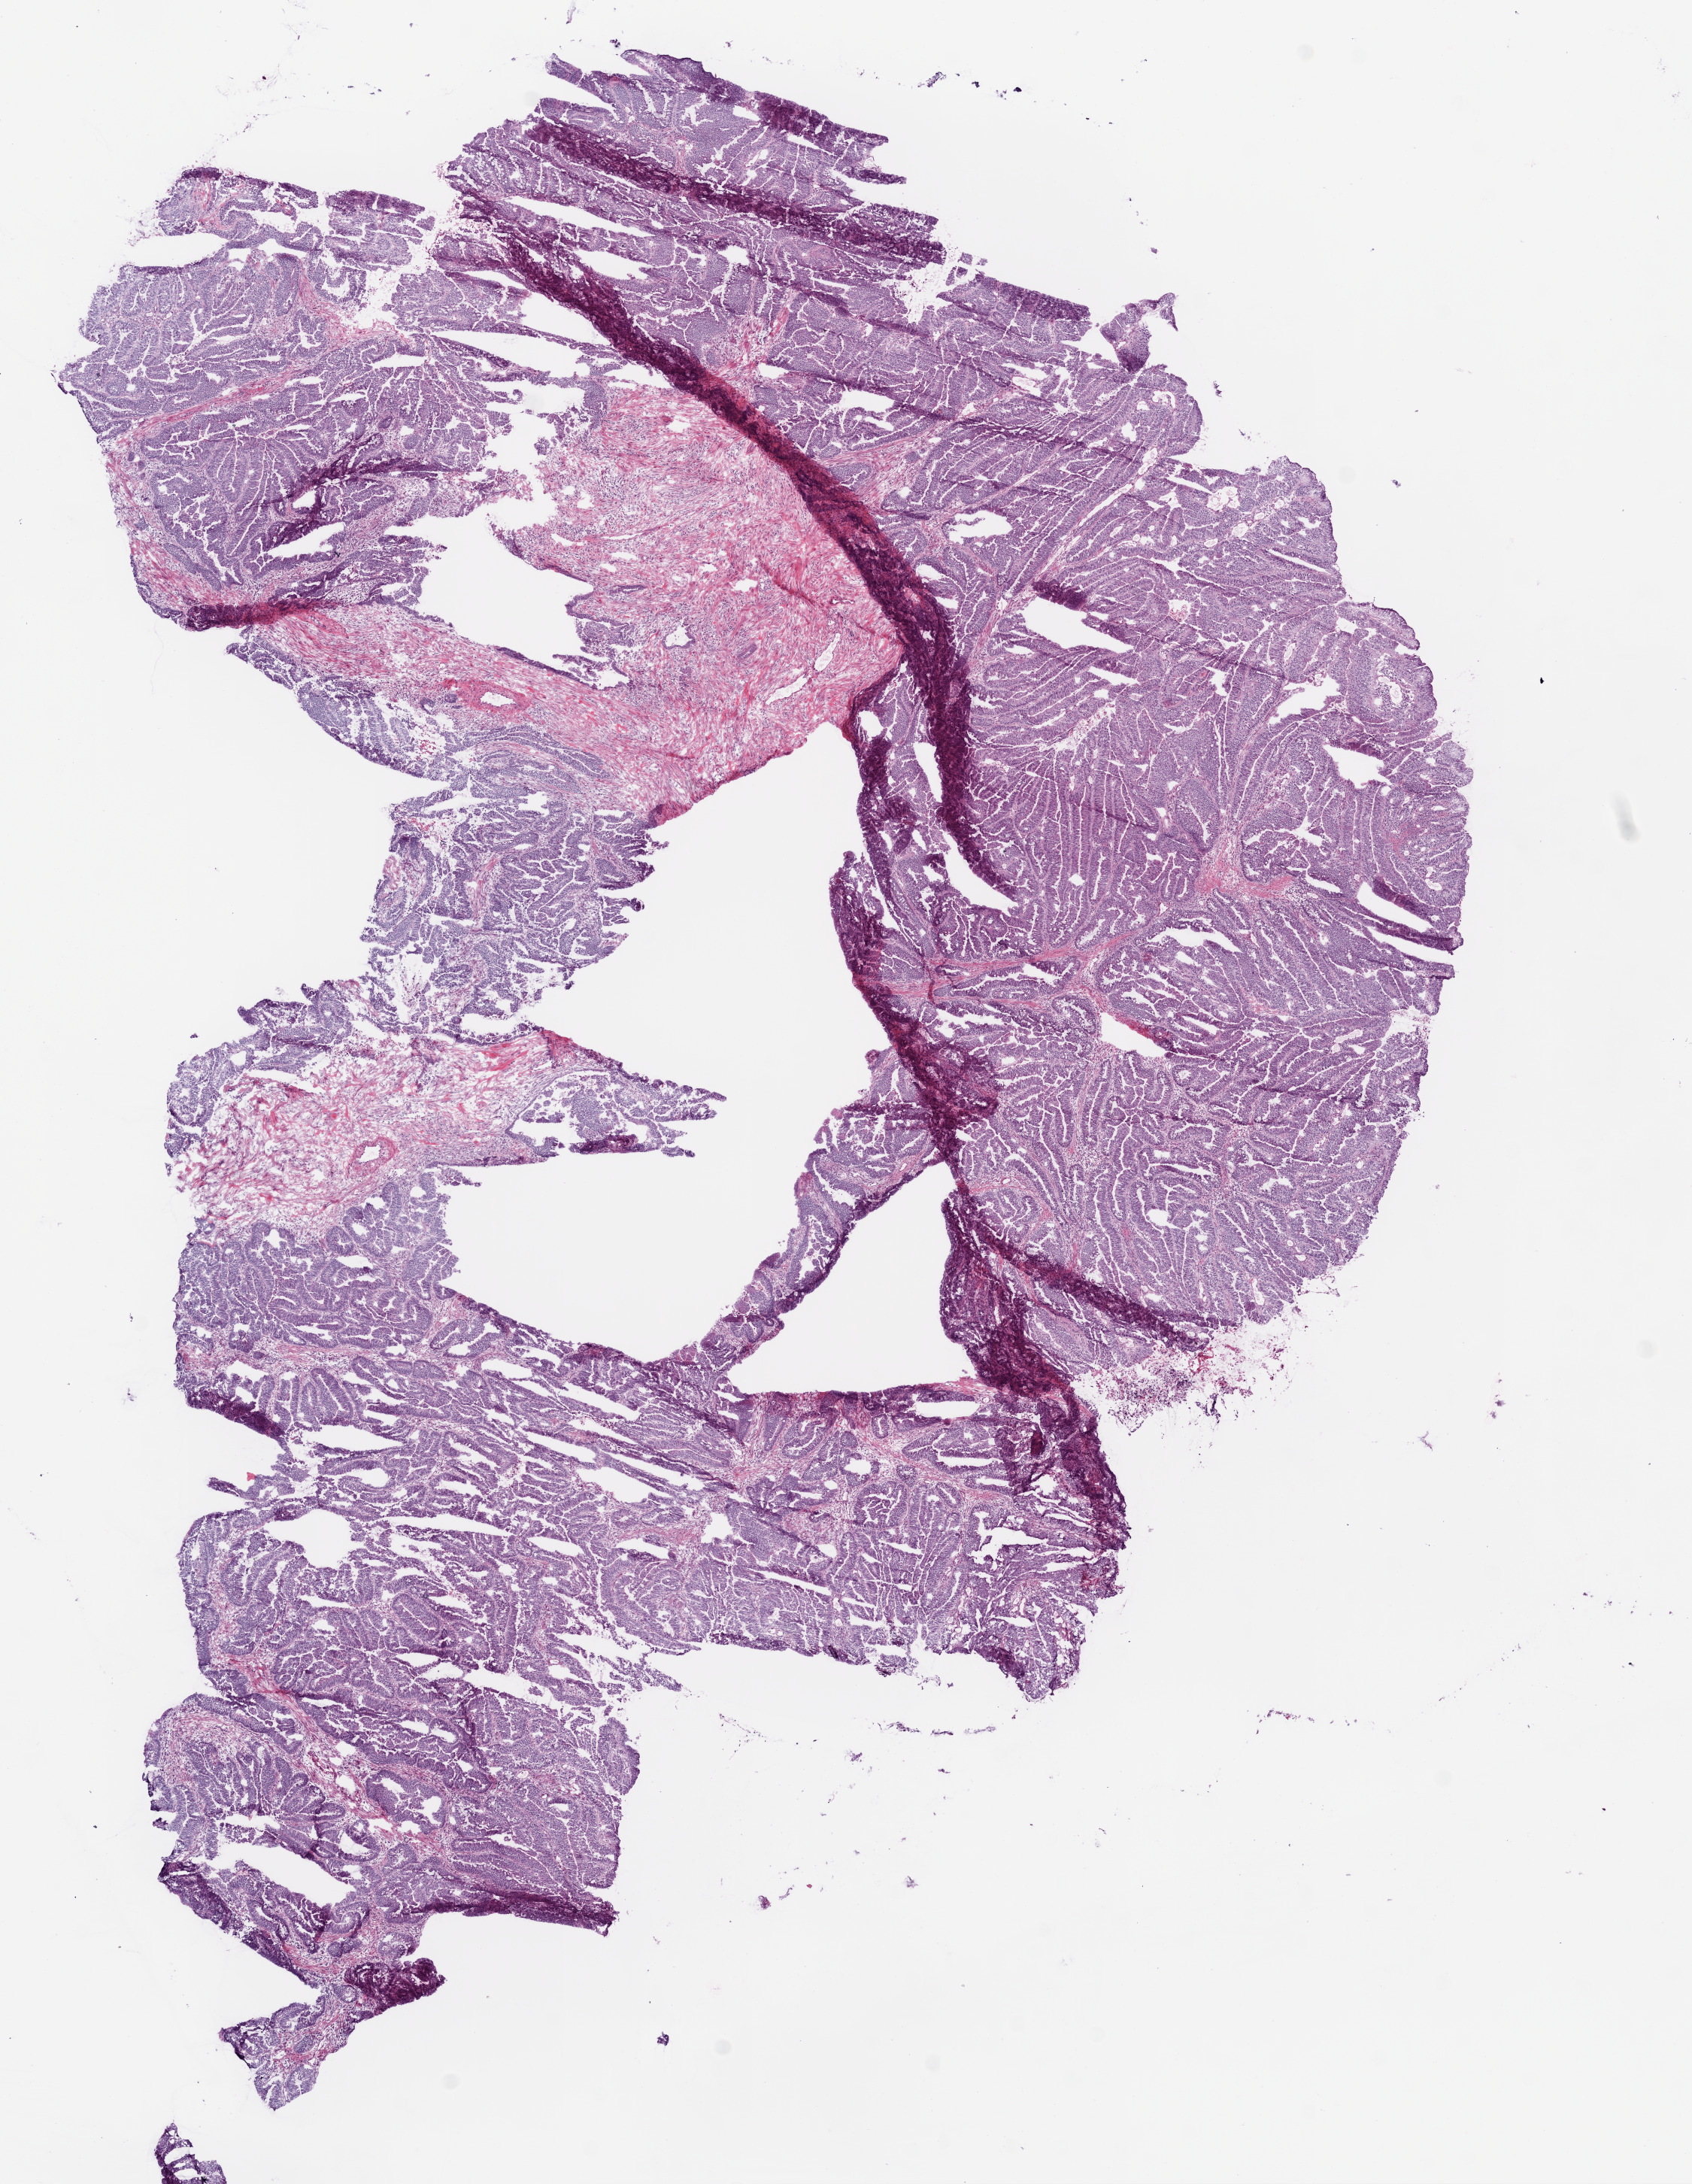
Digitized H&E-stained tissue section (whole slide) — low-resolution overview of the scanned area, about 9.0 x 11.7 mm; frozen section; sample: primary tumour, colon. Male patient; age at initial diagnosis 80 years. Slide review estimates, as recorded: tumour cells 80%, tumour nuclei 90%, normal cells 0%, stromal cells 20%, necrosis 0%.
AJCC pathologic stage: I. Pathologic diagnosis: Adenocarcinoma, NOS. Lymph nodes positive (case pathology): 0 of 24 examined.